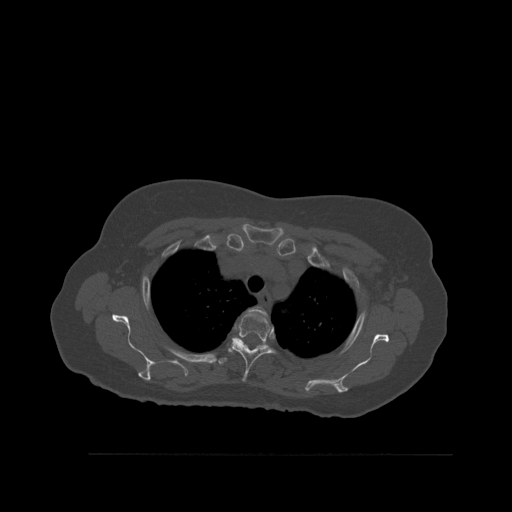
CT including the spine, one axial slice. Bone window (W 1800 / L 400 HU). 1.5 mm slice thickness. 512 × 512 image matrix, field of view 470 × 470 mm. Female patient, age 73 years. Case-level facts recorded for this patient, not image findings: primary cancer: breast.
Annotated regions visible in this slice (semi-automatic segmentation, software-assisted and operator-edited):
- T2 vertebra: bounding box [x1, y1, x2, y2] px = [249, 307, 267, 319]
- T3 vertebra: [229, 312, 274, 382]
- T4 vertebra: [218, 357, 228, 365]